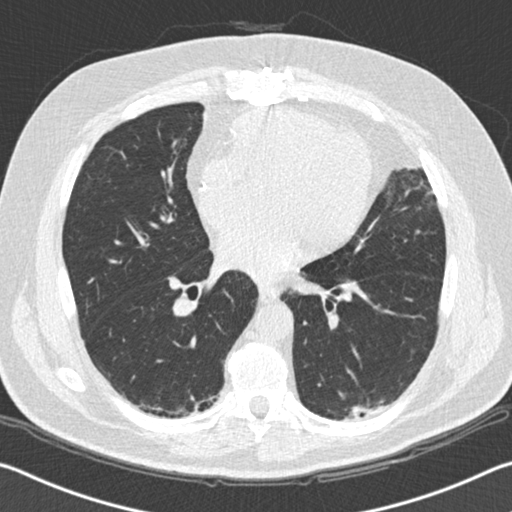
Low-dose screening chest CT, one axial slice; position 84 of 172 along the scan axis; reconstruction kernel B30f; lung window (W 1500 / L -600 HU); 512 × 512 image matrix.
Annotated regions visible in this slice (manually delineated by an expert):
- lesion 1 (tumor, lower lobe of left lung): box from (x=344, y=405) to (x=378, y=421) px